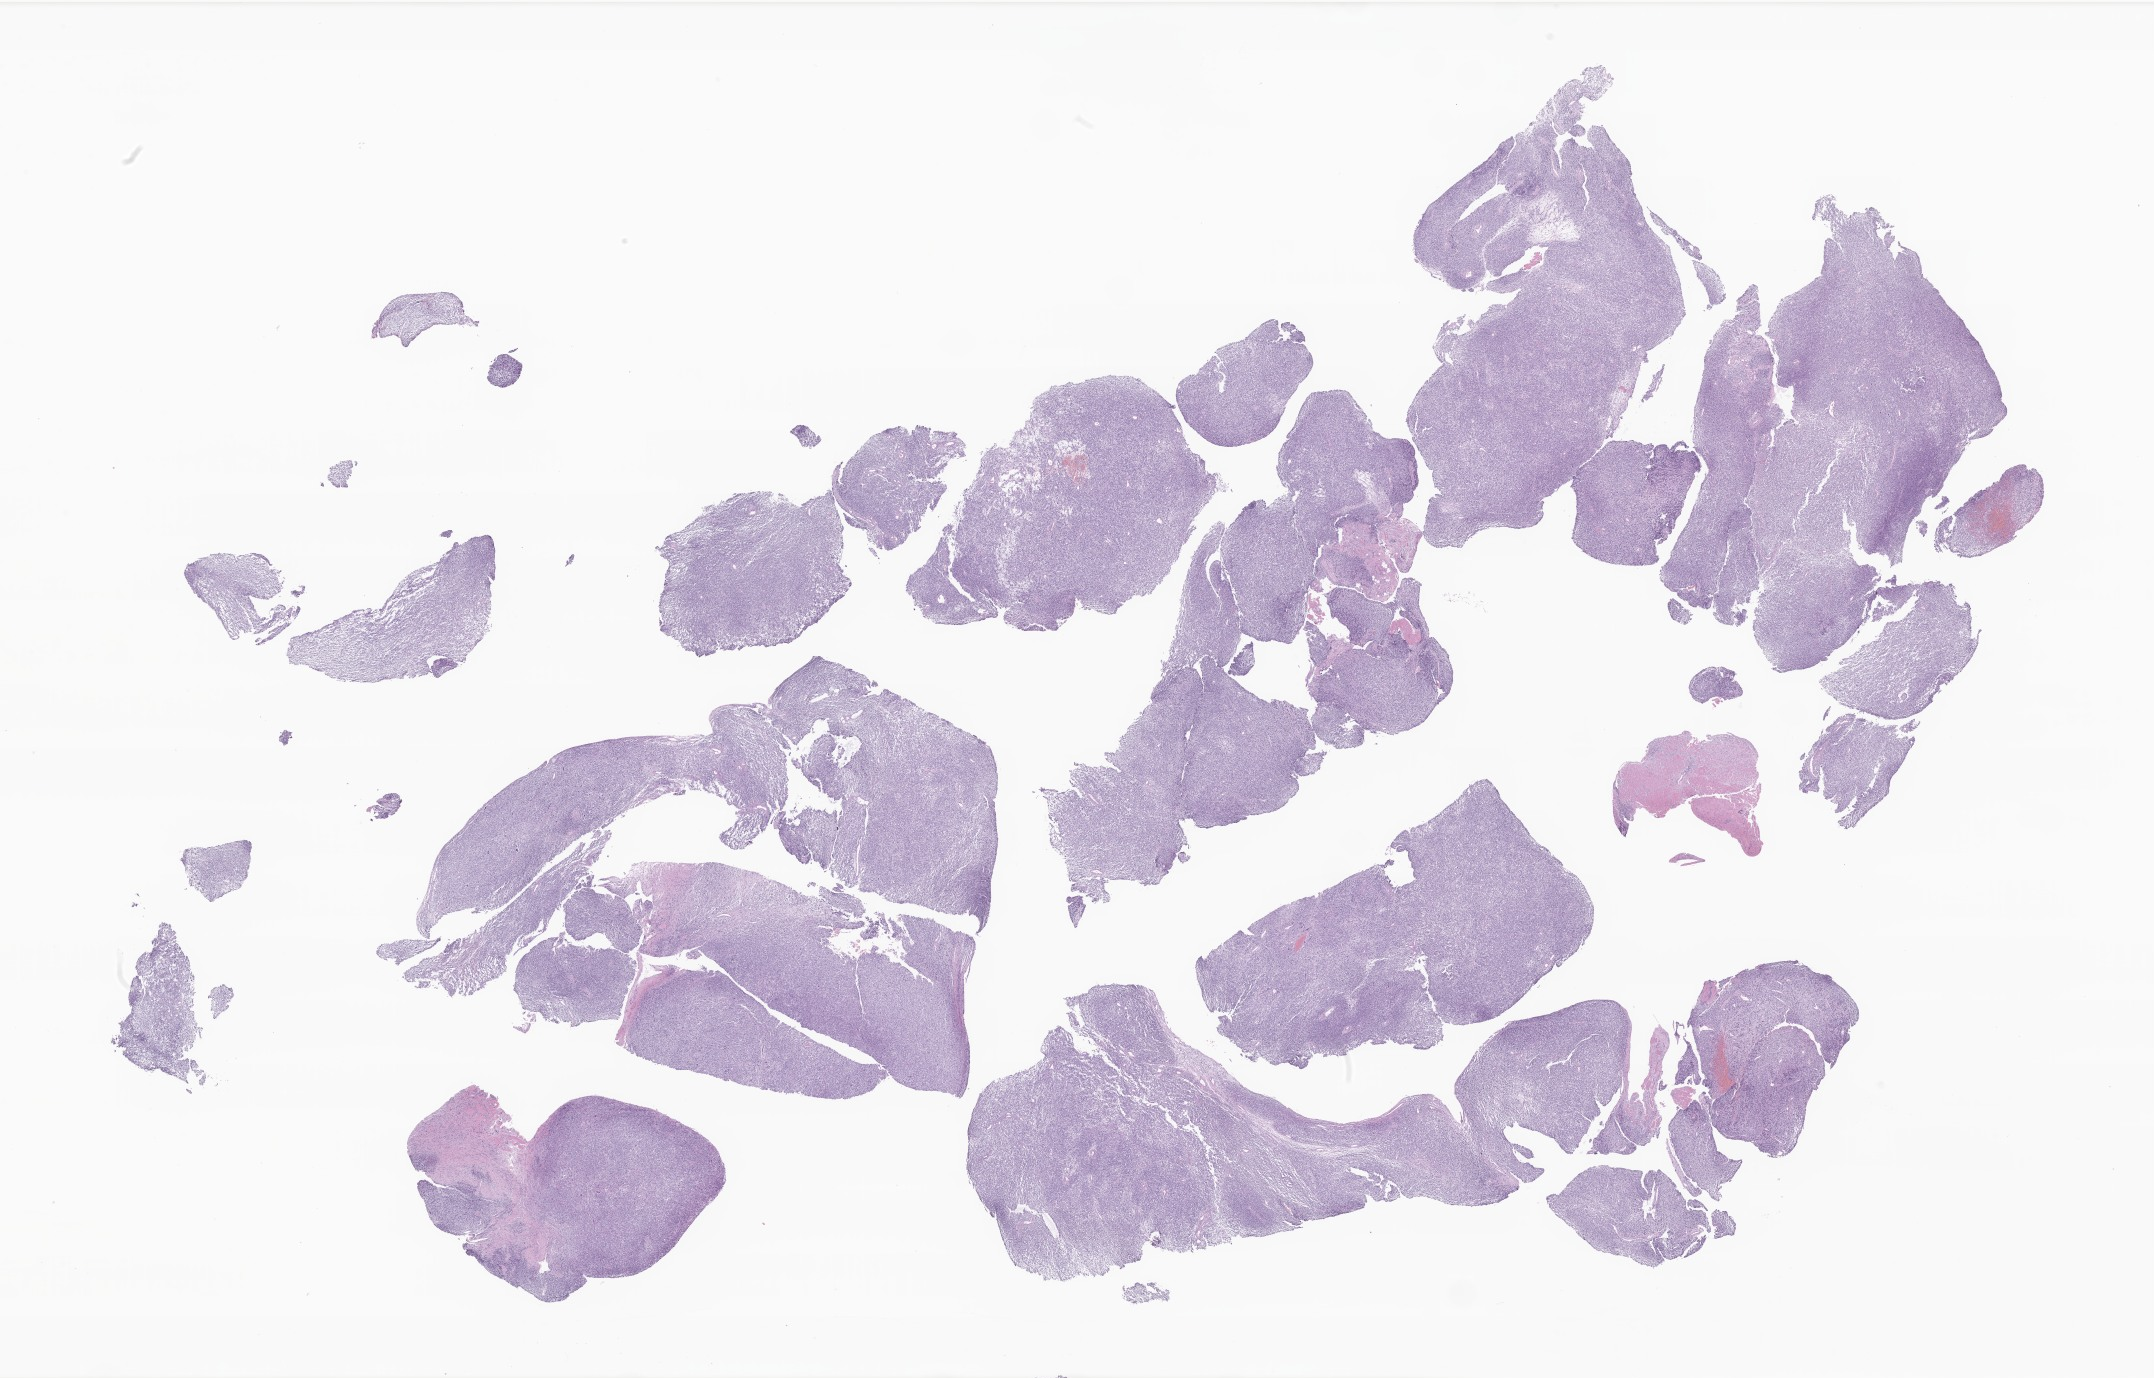
Haematoxylin and eosin whole-slide image of tumor tissue from the nerve of trunk — shown as a low-resolution overview of the whole scanned area (about 36.3 x 23.2 mm). FFPE section. Patient: female, age 379 days (about 1.0 years).
Diagnosis: Embryonal rhabdomyosarcoma, NOS.